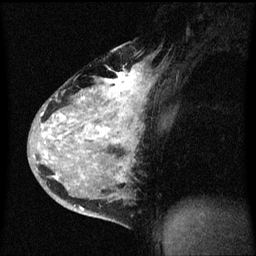
Breast MRI (dynamic contrast-enhanced), one sagittal slice. Position 39 of 60 along the scan axis. Dynamic contrast-enhanced series, image 2 of 3 at this slice position (ordered by acquisition). 1.5 T. TE 4.2 ms, TR 8.4 ms. 2 mm slice thickness. 256 × 256 image matrix. Patient: female, 34 years. Case-level facts recorded for this patient, not image findings: setting: breast cancer imaged before/during neoadjuvant chemotherapy; receptor status: HR-positive, HER2-negative.
Outlined on this slice (semi-automatically segmented with operator editing):
- analysis volume of interest (the breast-tissue region the enhancement analysis was run in; not a lesion): bounding box (x1, y1, x2, y2) in pixels: (34, 48, 153, 215)
- tumour enhancement mask (voxels above the 70 % enhancement threshold inside the analysis volume of interest): (40, 70, 141, 211)